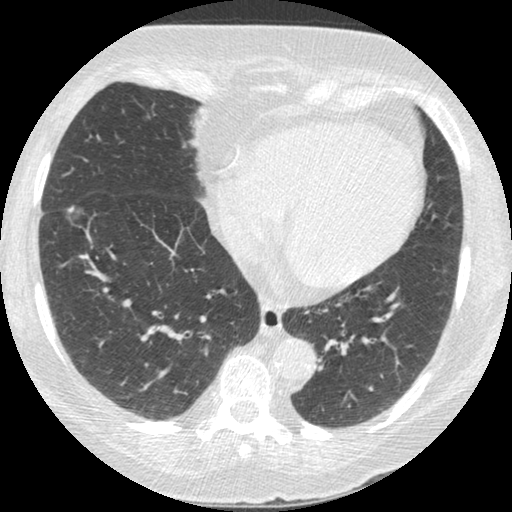
Low-dose screening chest CT, one axial slice. Slice 97 of 245 in the series (ordered by position). 120 kVp. Lung window (W 1500 / L -600 HU). 1.25 mm slice thickness. 512 × 512 image matrix, field of view 310 × 310 mm.
Outlined on this slice (expert manual segmentation):
- lesion 1 (tumor, lower lobe of right lung): bounding box [x1, y1, x2, y2] px = [67, 206, 79, 216]